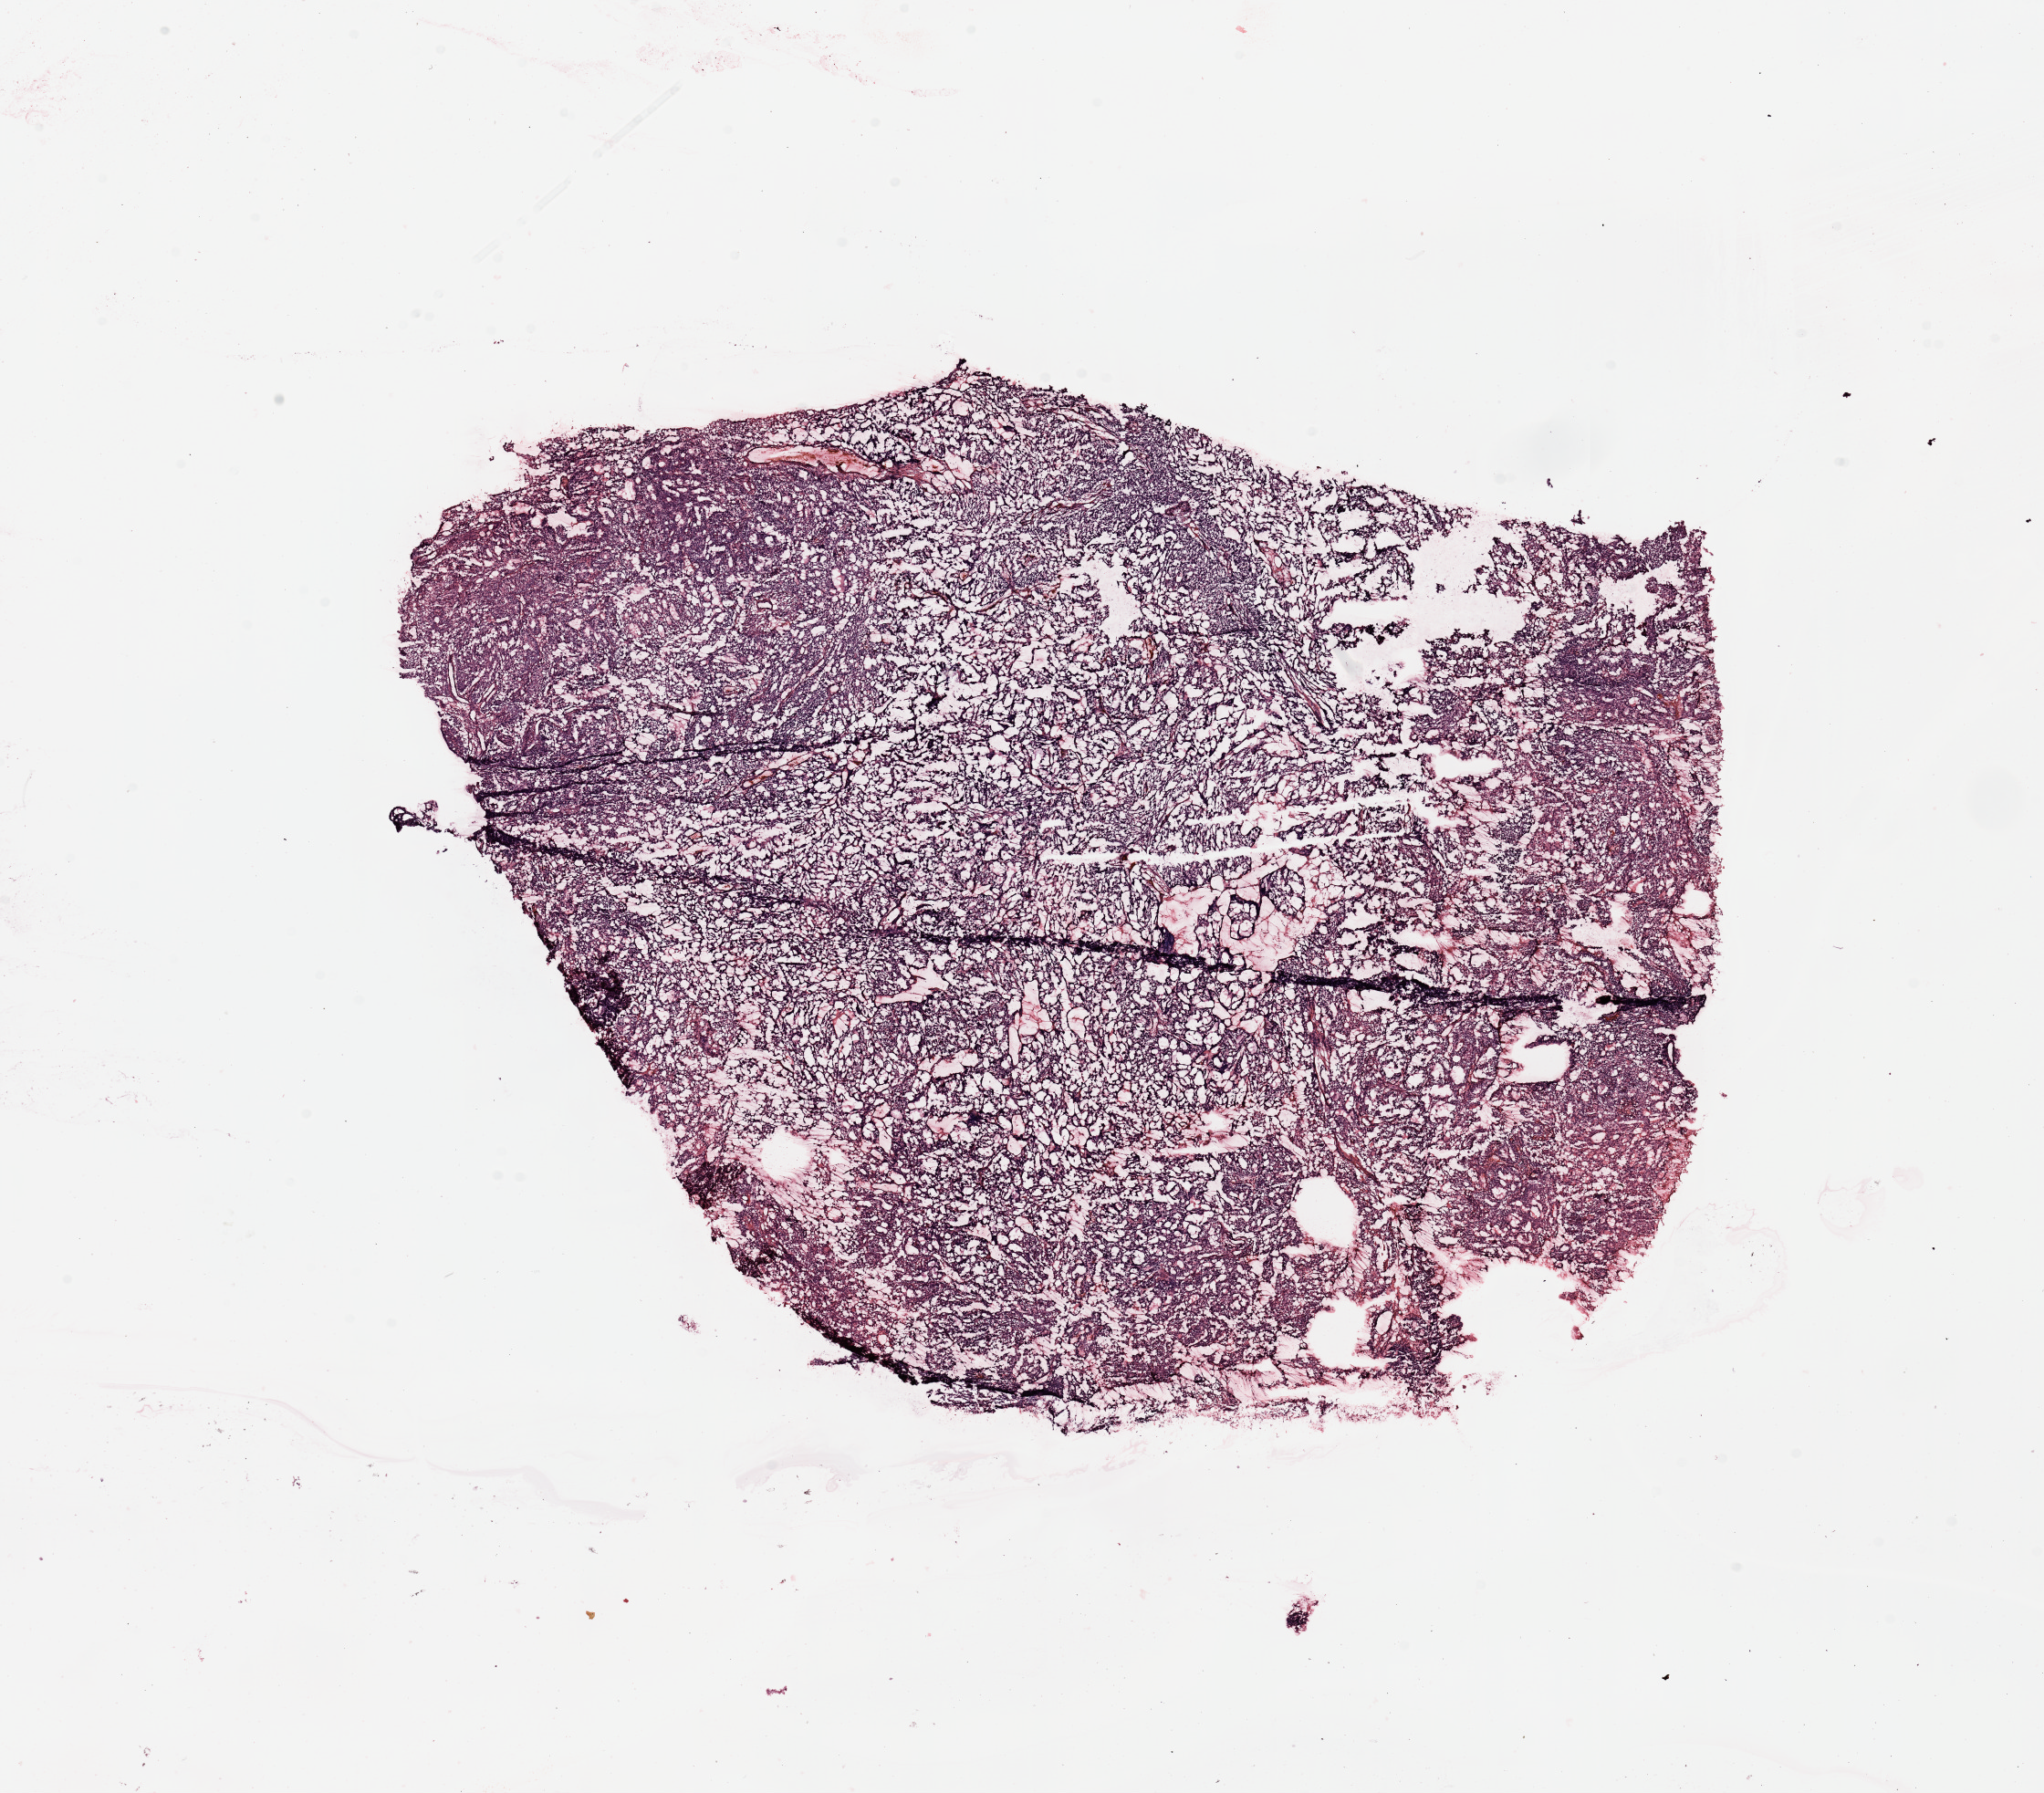
Whole-slide histology image, H&E-stained — whole scanned area (about 17.7 x 15.5 mm, from a 20x scan) shown as a low-resolution overview, uterus, tumour tissue. Patient: female, age 67 years.
Histologic diagnosis: Endometrioid adenocarcinoma, NOS.